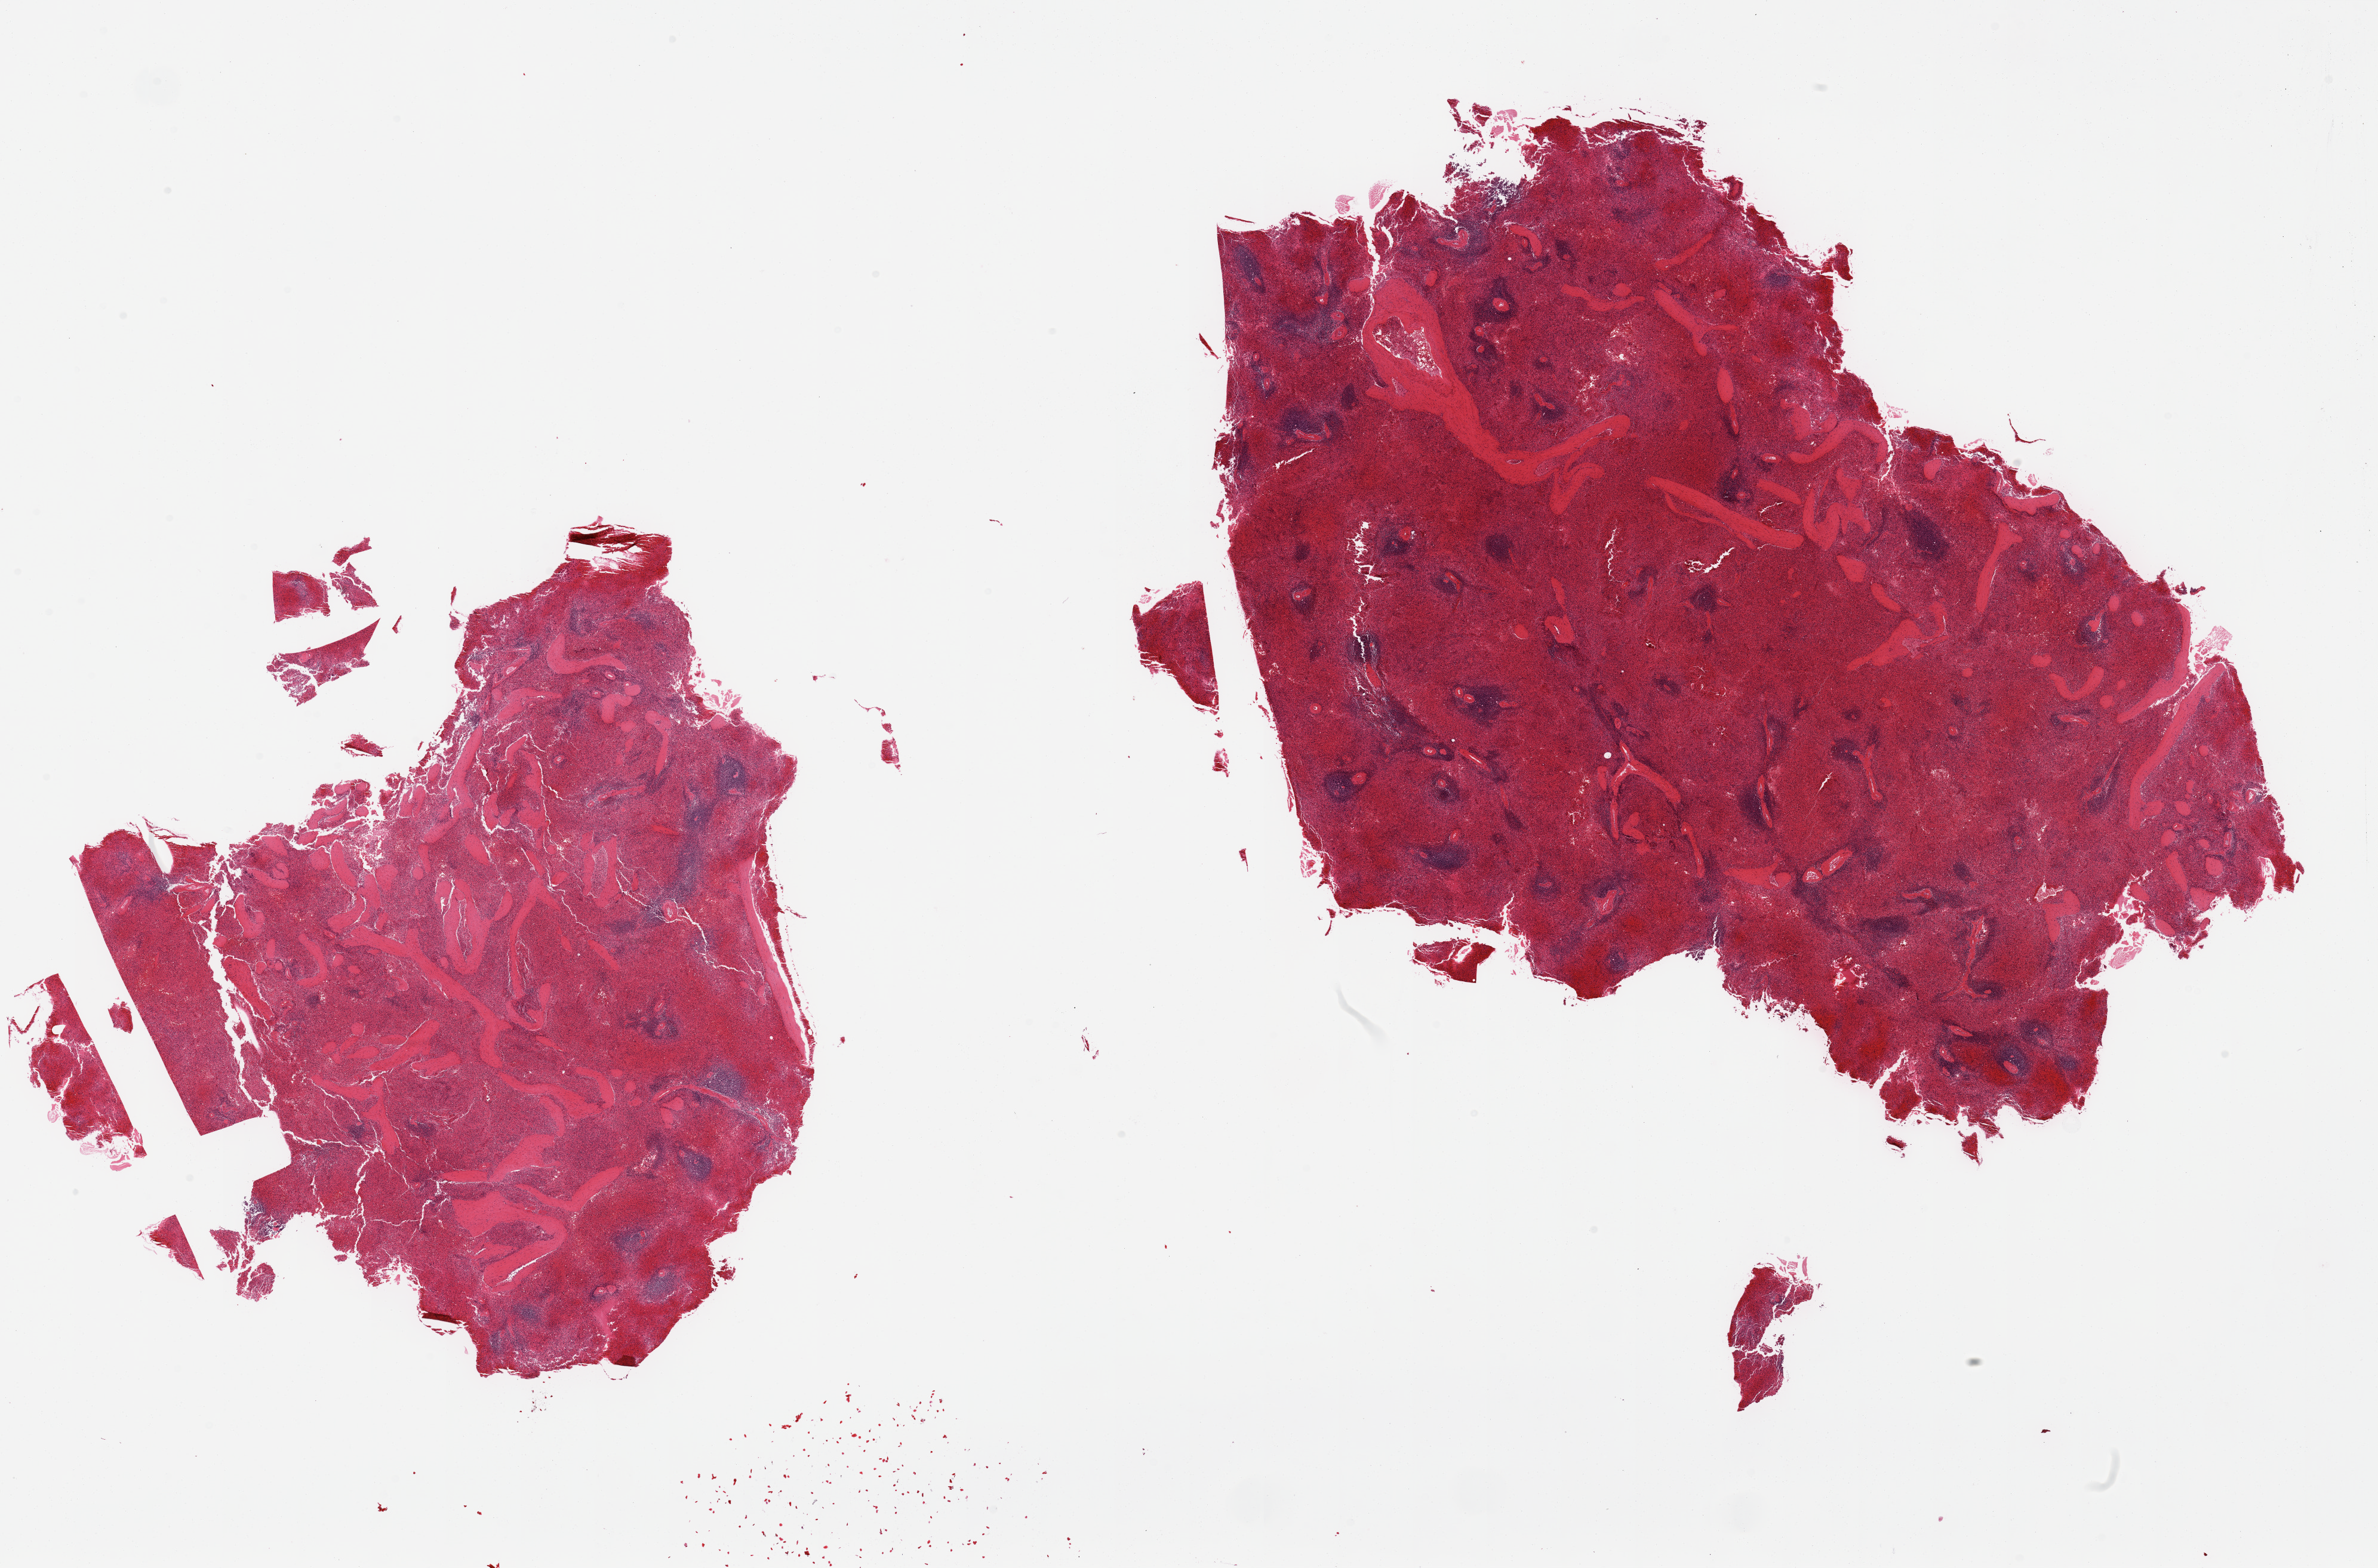
Digitized H&E-stained section, brightfield — a low-resolution overview of the entire scanned area, about 31.5 x 20.8 mm; PAXgene-fixed, paraffin-embedded tissue; sampled site (target tissue): spleen; donor tissue sample. Donor: male.
Review note (as recorded): 2 pieces; moderately congested.